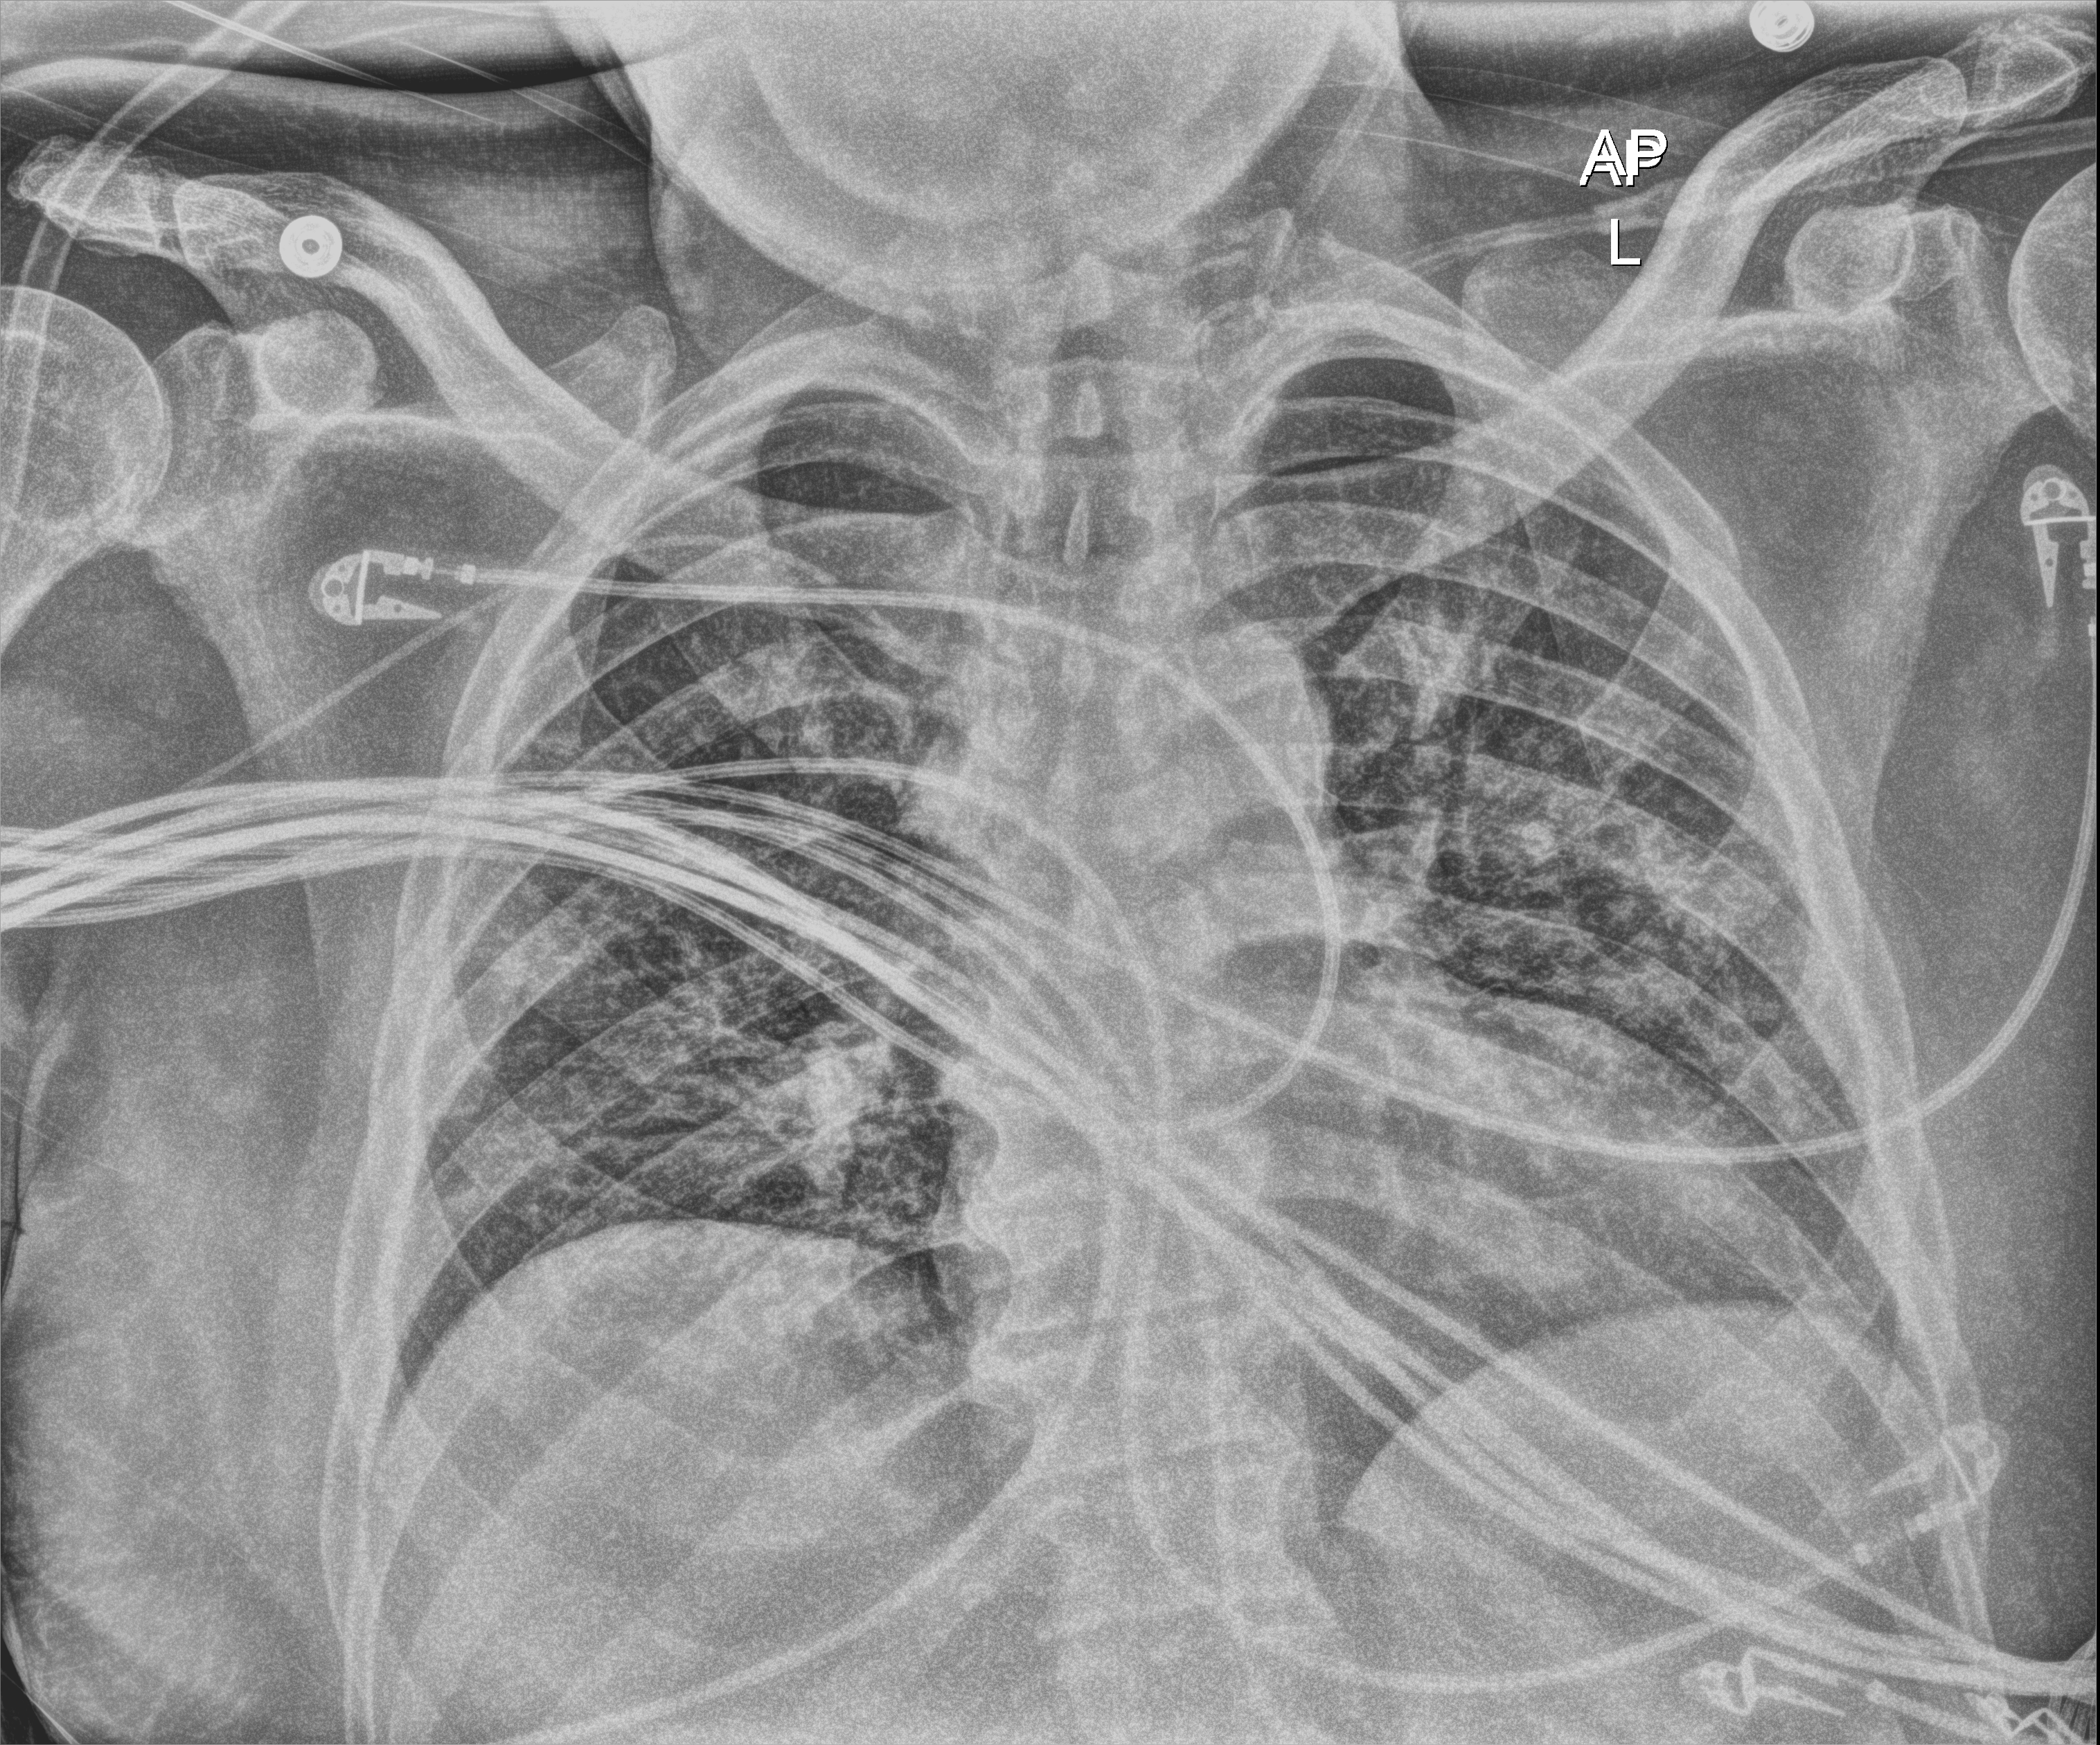
Portable chest radiograph; anteroposterior (AP) projection. Male patient hospitalised with COVID-19, age 18–59 years.
Hospital-stay facts (about this admission, not read from this image; timing relative to this image not recorded): length of hospital stay: 41 days.